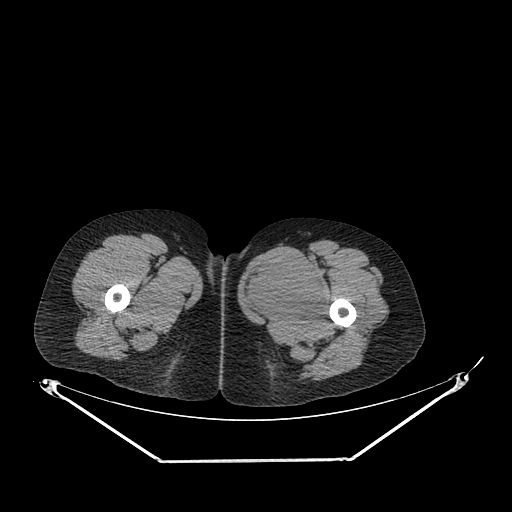
CT of an extremity soft-tissue mass (from a PET/CT study), one axial slice. Position 247 of 267 along the scan axis. Reconstruction kernel SOFT. 120 kVp. Soft-tissue window (W 400 / L 40 HU). 512 × 512 image matrix. Female patient. Case-level facts recorded for this patient, not image findings: histological type: pleiomorphic leiomyosarcoma; grade: intermediate; site of the primary tumour: left thigh.
Outlined on this slice (expert contour drawn on MRI and transferred to this co-registered scan by the dataset authors):
- gross tumour volume including surrounding oedema: bounding box <242,256,325,323> (left, top, right, bottom; pixels)
- gross tumour volume (mass): <242,256,325,323>